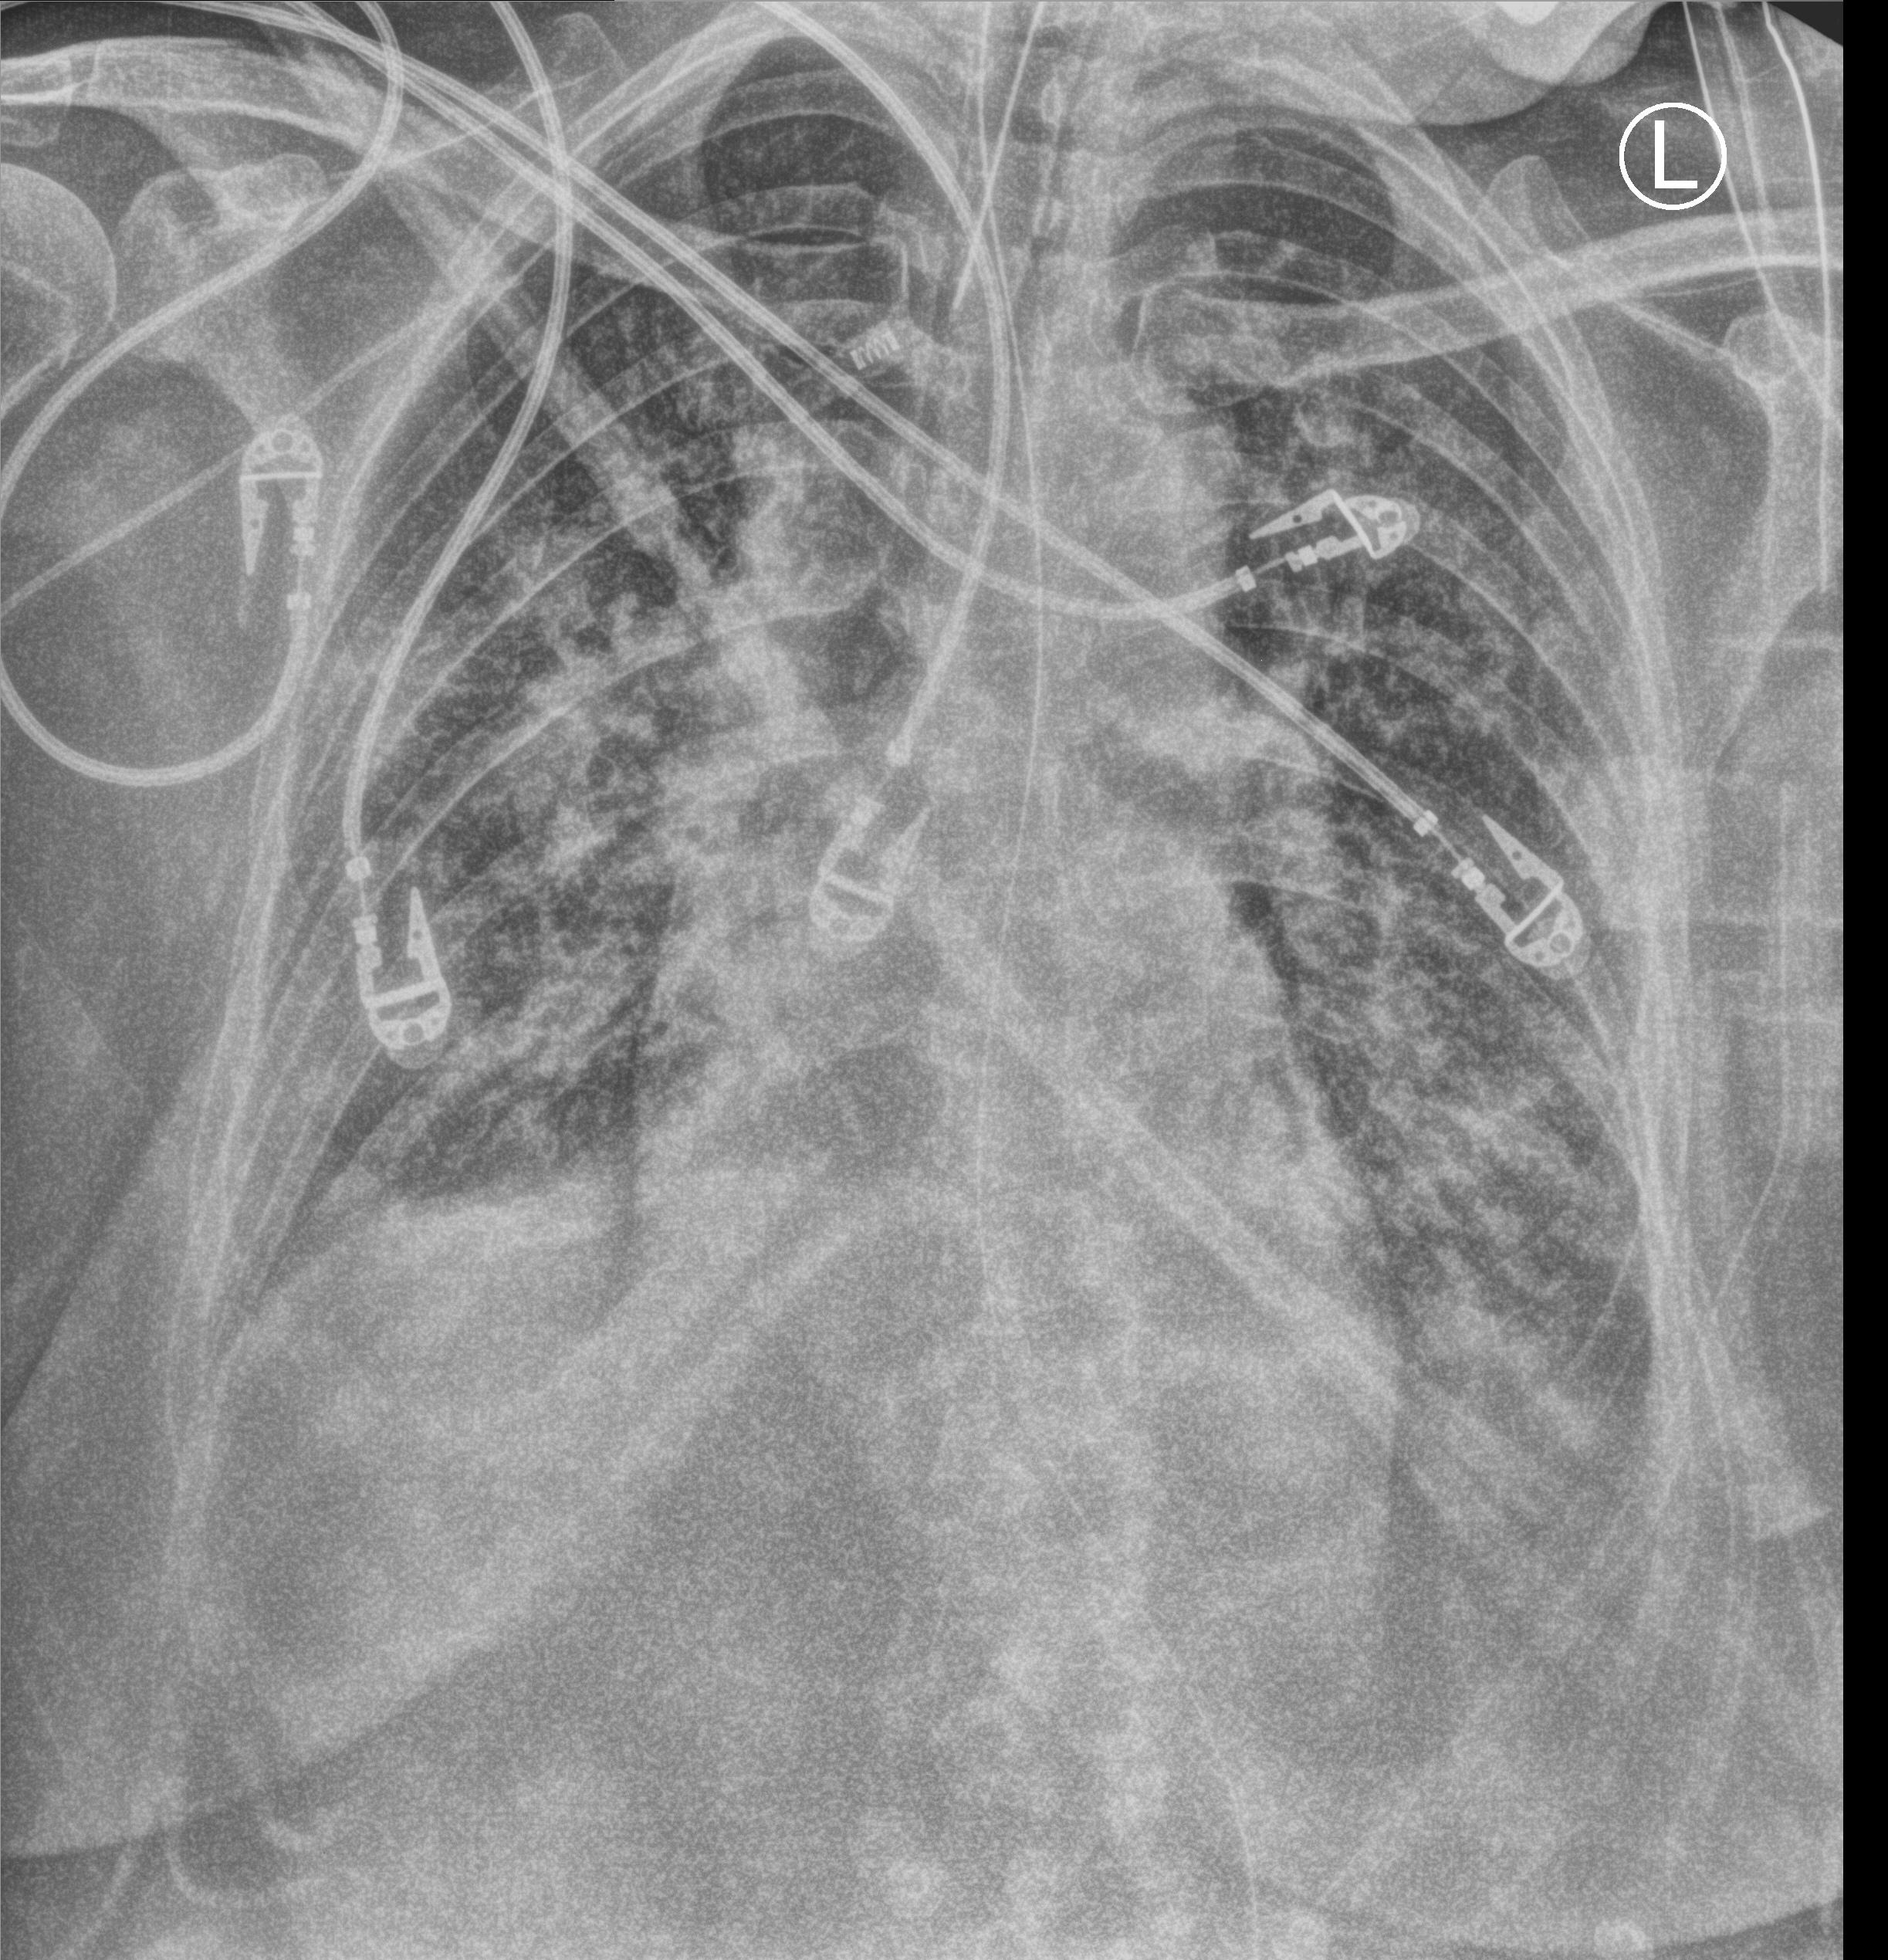
Portable chest radiograph, anteroposterior (AP) projection. Patient hospitalised with COVID-19; female, aged 18–59 years.
From the hospital-stay record, not from the radiograph (when in the stay this image was taken is not recorded):
- admitted to intensive care during this hospital stay: yes
- mechanically ventilated during this hospital stay: yes